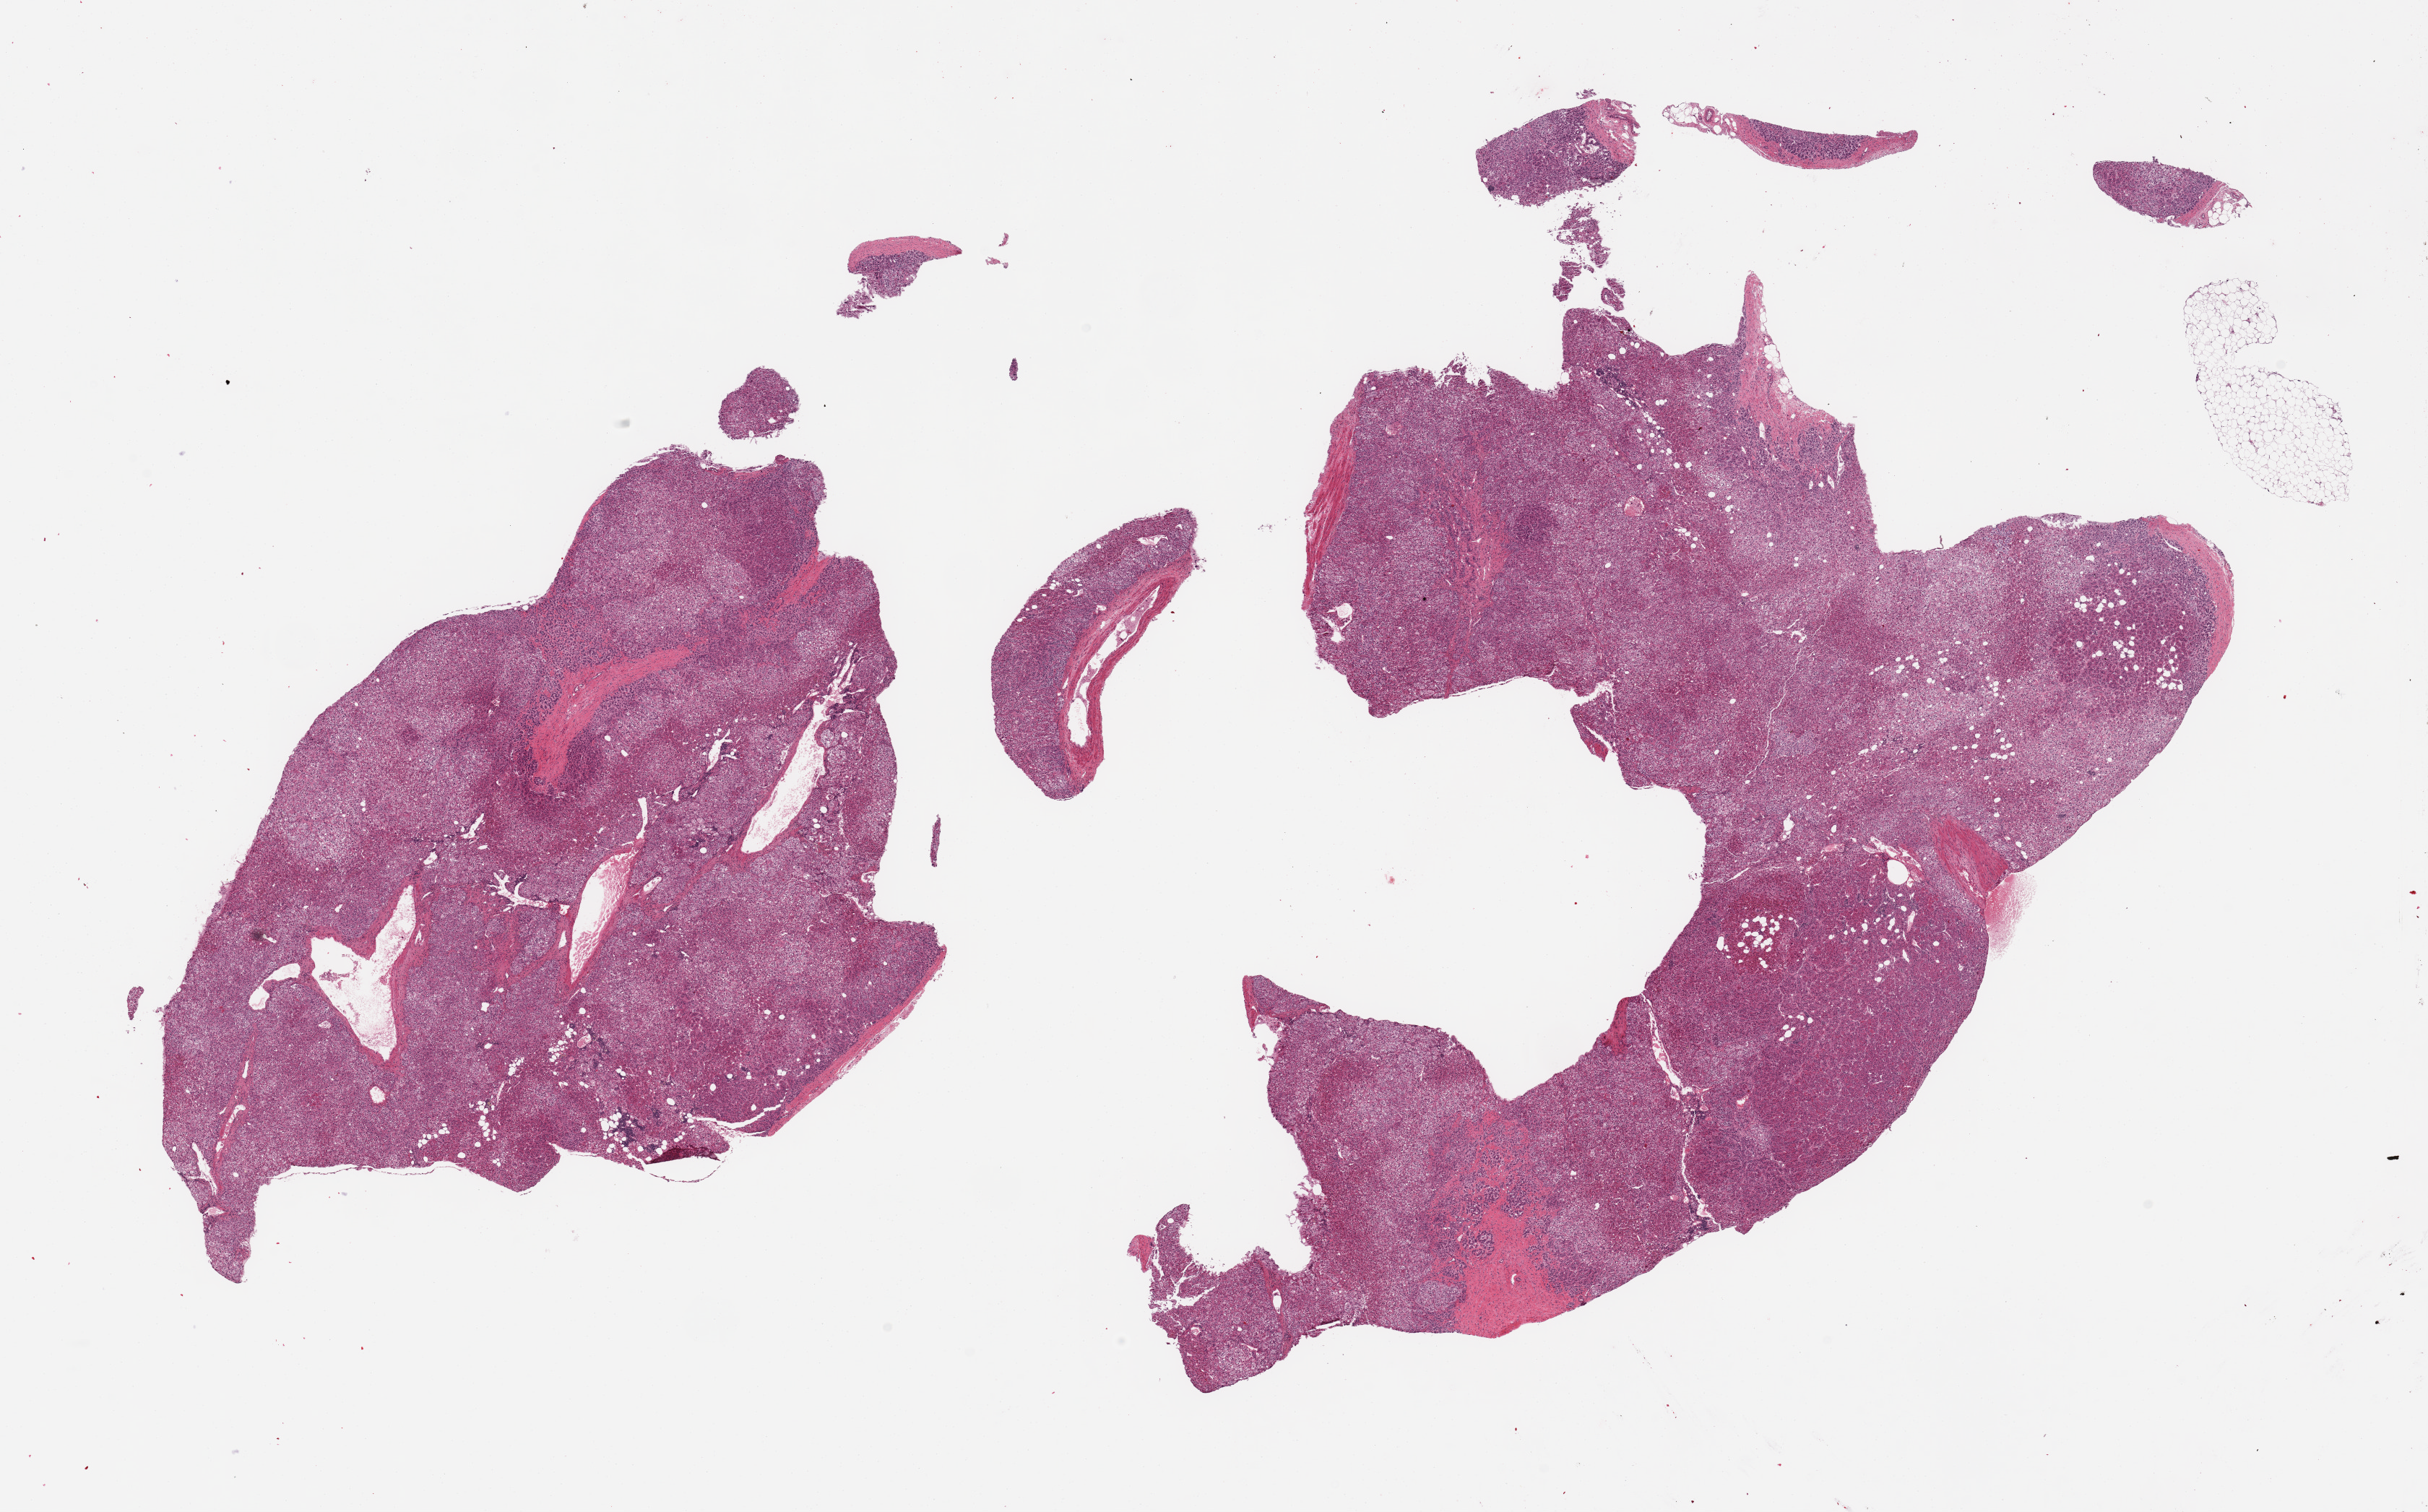
Hematoxylin and eosin (H&E) whole-slide image, low-resolution overview of the scanned area, about 26.6 x 16.6 mm; PAXgene-fixed paraffin-embedded (PFPE) section; target tissue: adrenal gland; donor tissue sample. Donor sex: female.
Review note (as recorded): 2 pieces, cortex, well-preserved.